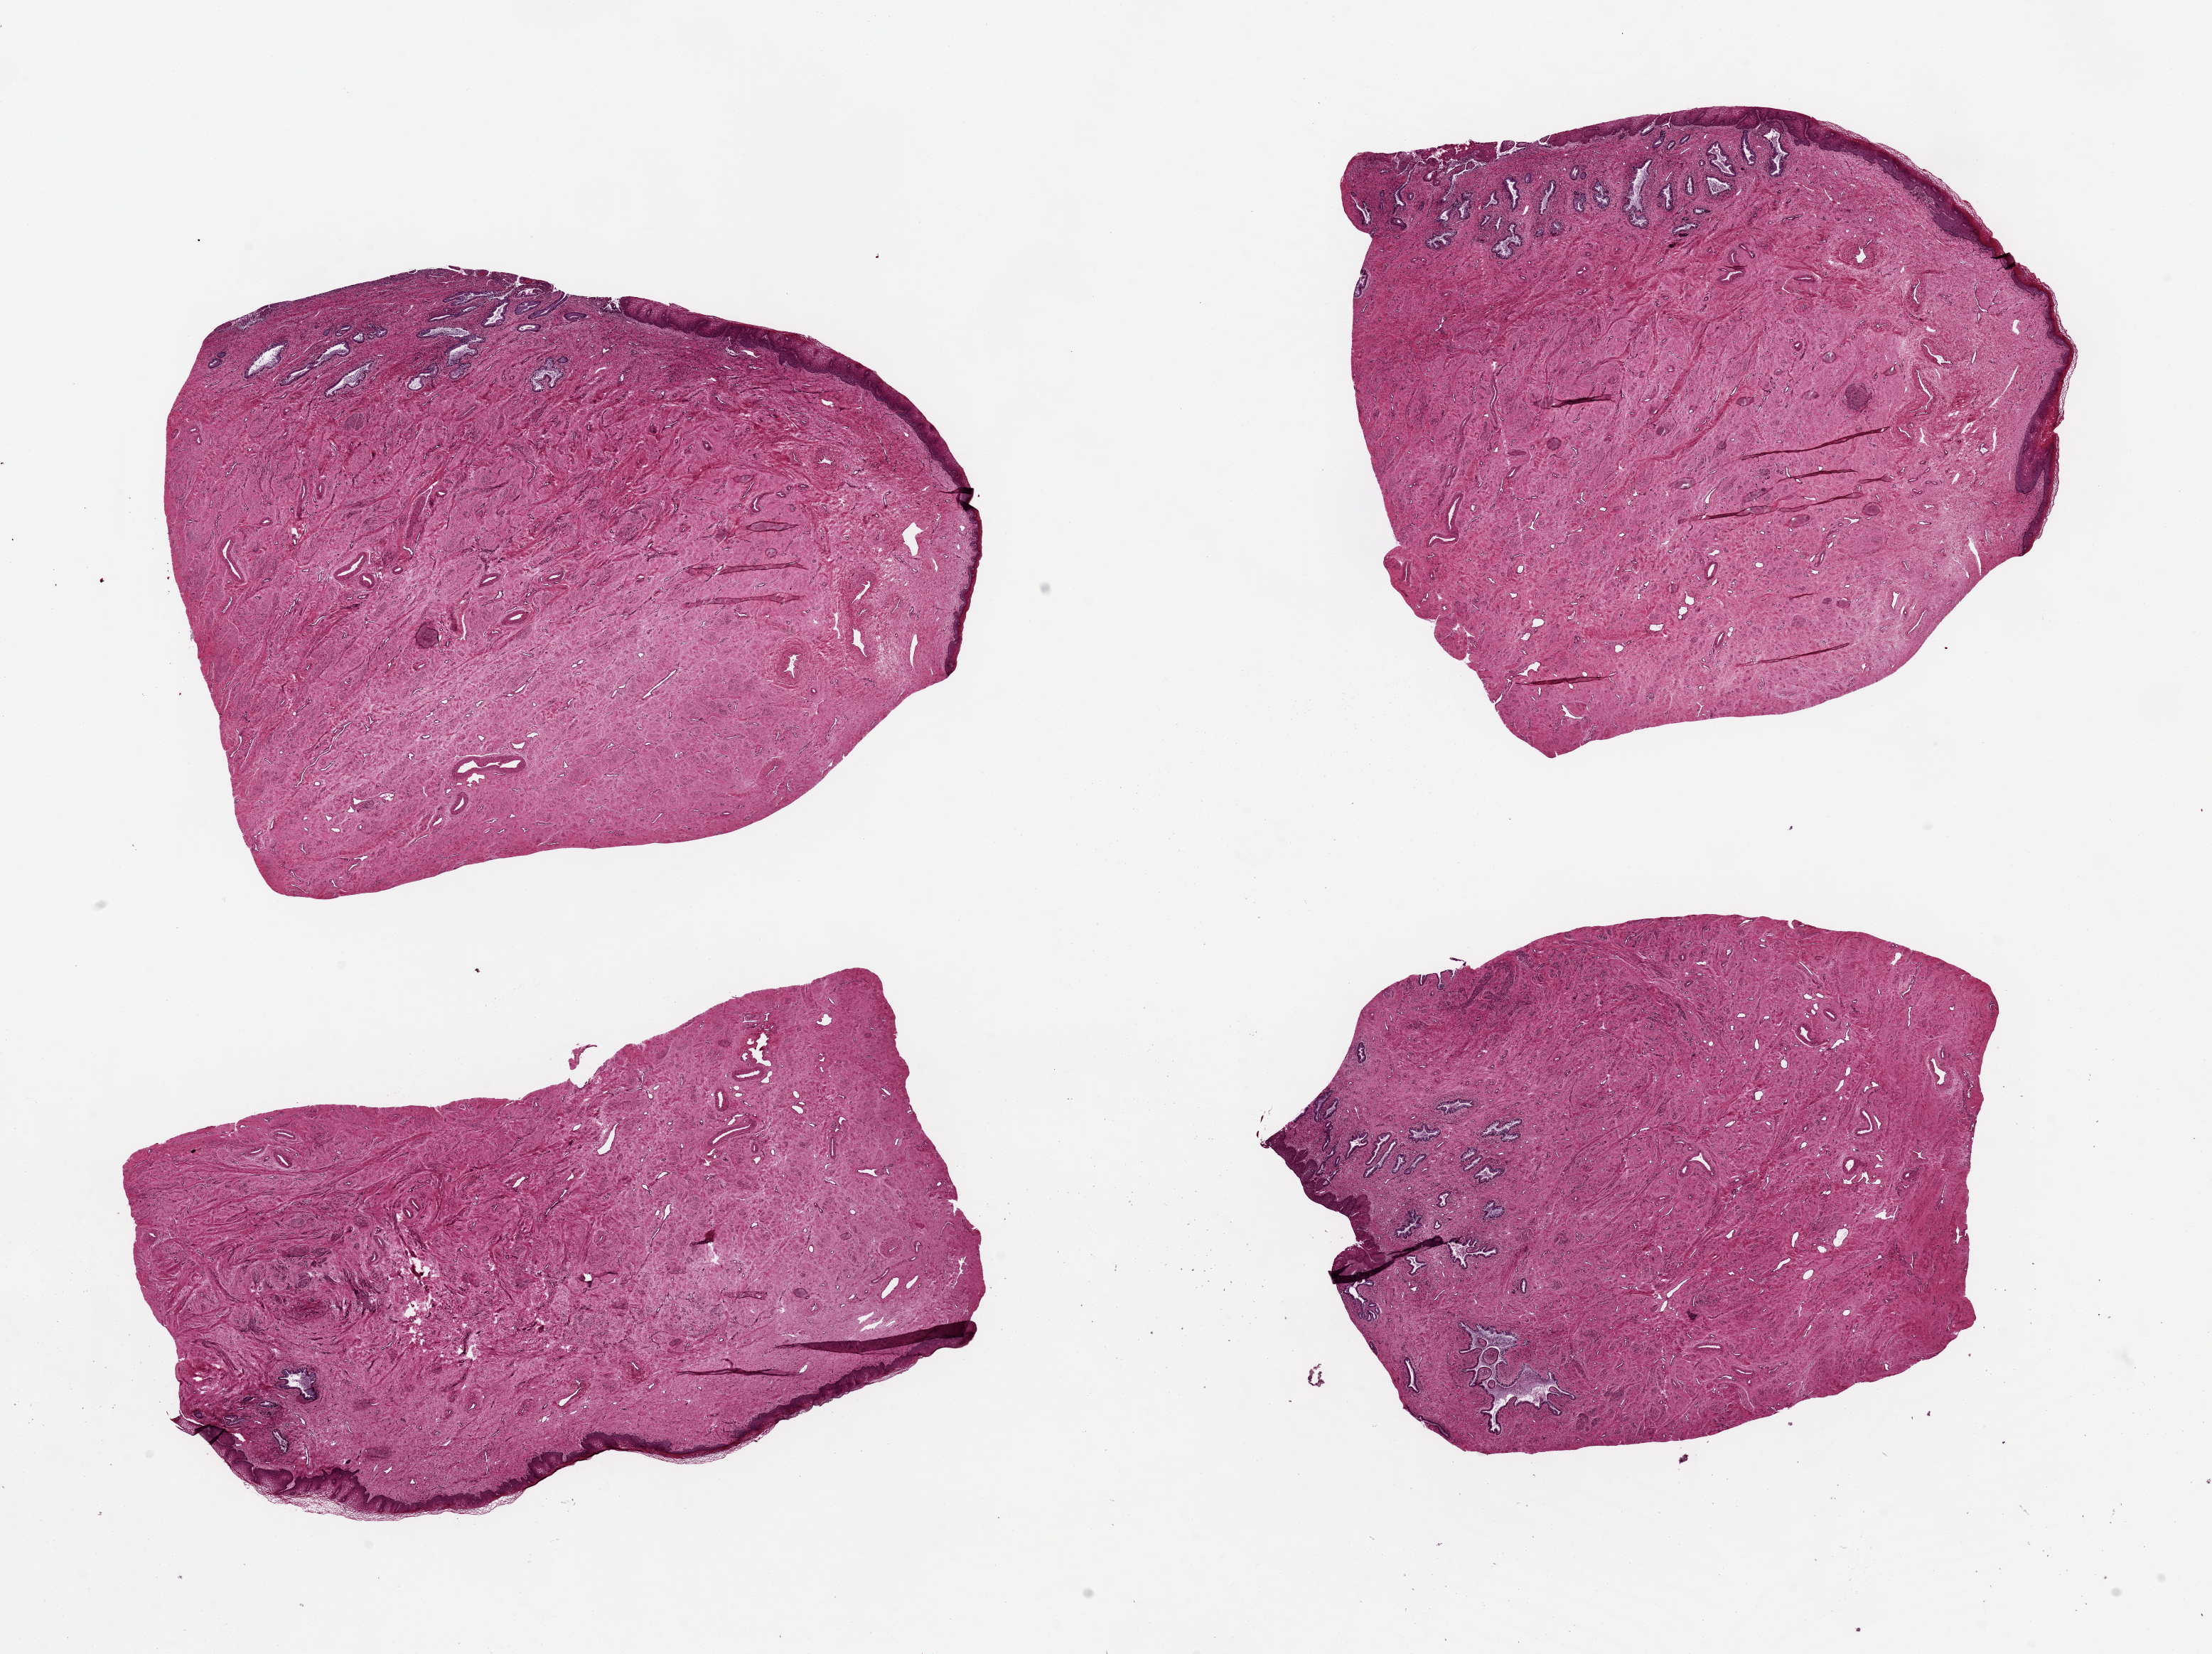
Digitized haematoxylin and eosin-stained section, brightfield — low-resolution overview of the scanned area, about 24.6 x 18.4 mm; PAXgene-fixed paraffin-embedded (PFPE) section; section of exocervix (target tissue); donor tissue sample. Donor sex: female.
Reviewer comment on this tissue sample: 6 pieces, ~ 8x6mm both endo and ectocervial mucosa, well preserved, representative endocervical glands.